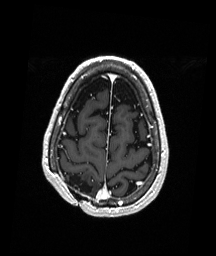
Brain MRI from a brain-tumour surgery series, one axial slice; slice 51 of 192 in the series (ordered by position); T1-weighted post-contrast; 1 mm slice thickness; 216 × 256 image matrix, field of view 211 × 250 mm. From the clinical record (not read from this slice): histopathology: Astrocytoma; WHO grade: 3; IDH mutation: yes; tumour location: Right Parietal.
Structures marked on this image (outlined manually by an expert reader):
- previous resection cavity: box from (x=64, y=173) to (x=93, y=193) px